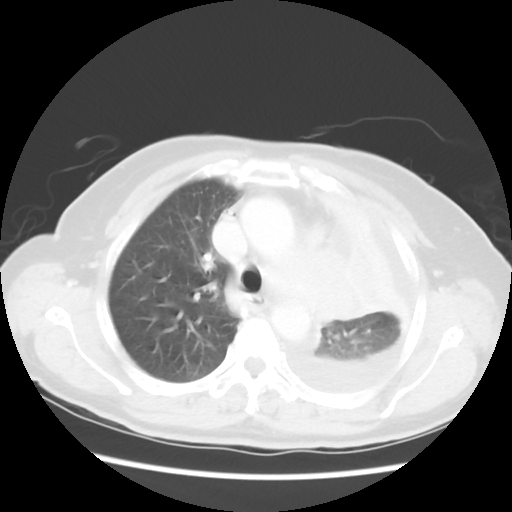
Chest CT, one axial slice; position 38 of 52 along the scan axis; 120 kVp; lung window (W 1500 / L -600 HU); 512 × 512 image matrix. Female patient, age 72 years. Case-level facts recorded for this patient, not image findings: clinical TNM (as recorded): T4 N3 M1b; histopathological grade: G3.
Annotated regions visible in this slice (bounding box drawn by a radiologist):
- lung tumour (recorded histology: large cell carcinoma): bounding box (x1, y1, x2, y2) in pixels: (300, 242, 363, 334)